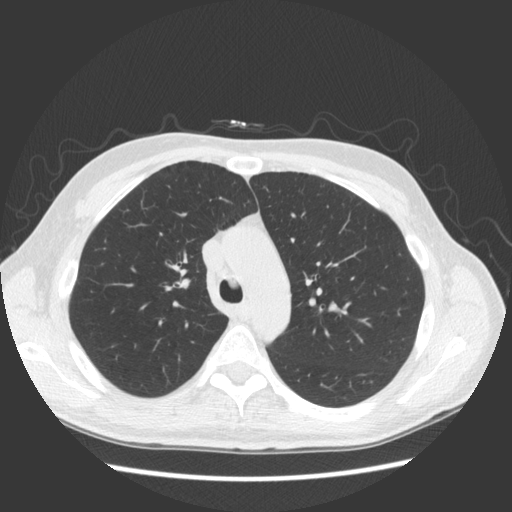
Low-dose screening chest CT, axial slice. Second screening round (one year after baseline). Lung window (W 1500 / L -600 HU). Slice 52 of 163 in the series. 512 × 512 image matrix. Male, age 57 years at enrolment. Former smoker at enrolment.
- Expert-annotated lung lesion, box from (x=151, y=244) to (x=204, y=303) px.
- The screening reader recorded 3 non-calcified nodules or masses ≥4 mm on this exam (right middle lobe, right middle lobe, right middle lobe); which of them this box marks is not recorded.
- Participant outcome: lung cancer diagnosed 264 days after this screen — adenocarcinoma, NOS, right upper lobe, poorly differentiated (G3), stage IB (AJCC 6th edition), 25 mm at pathology.